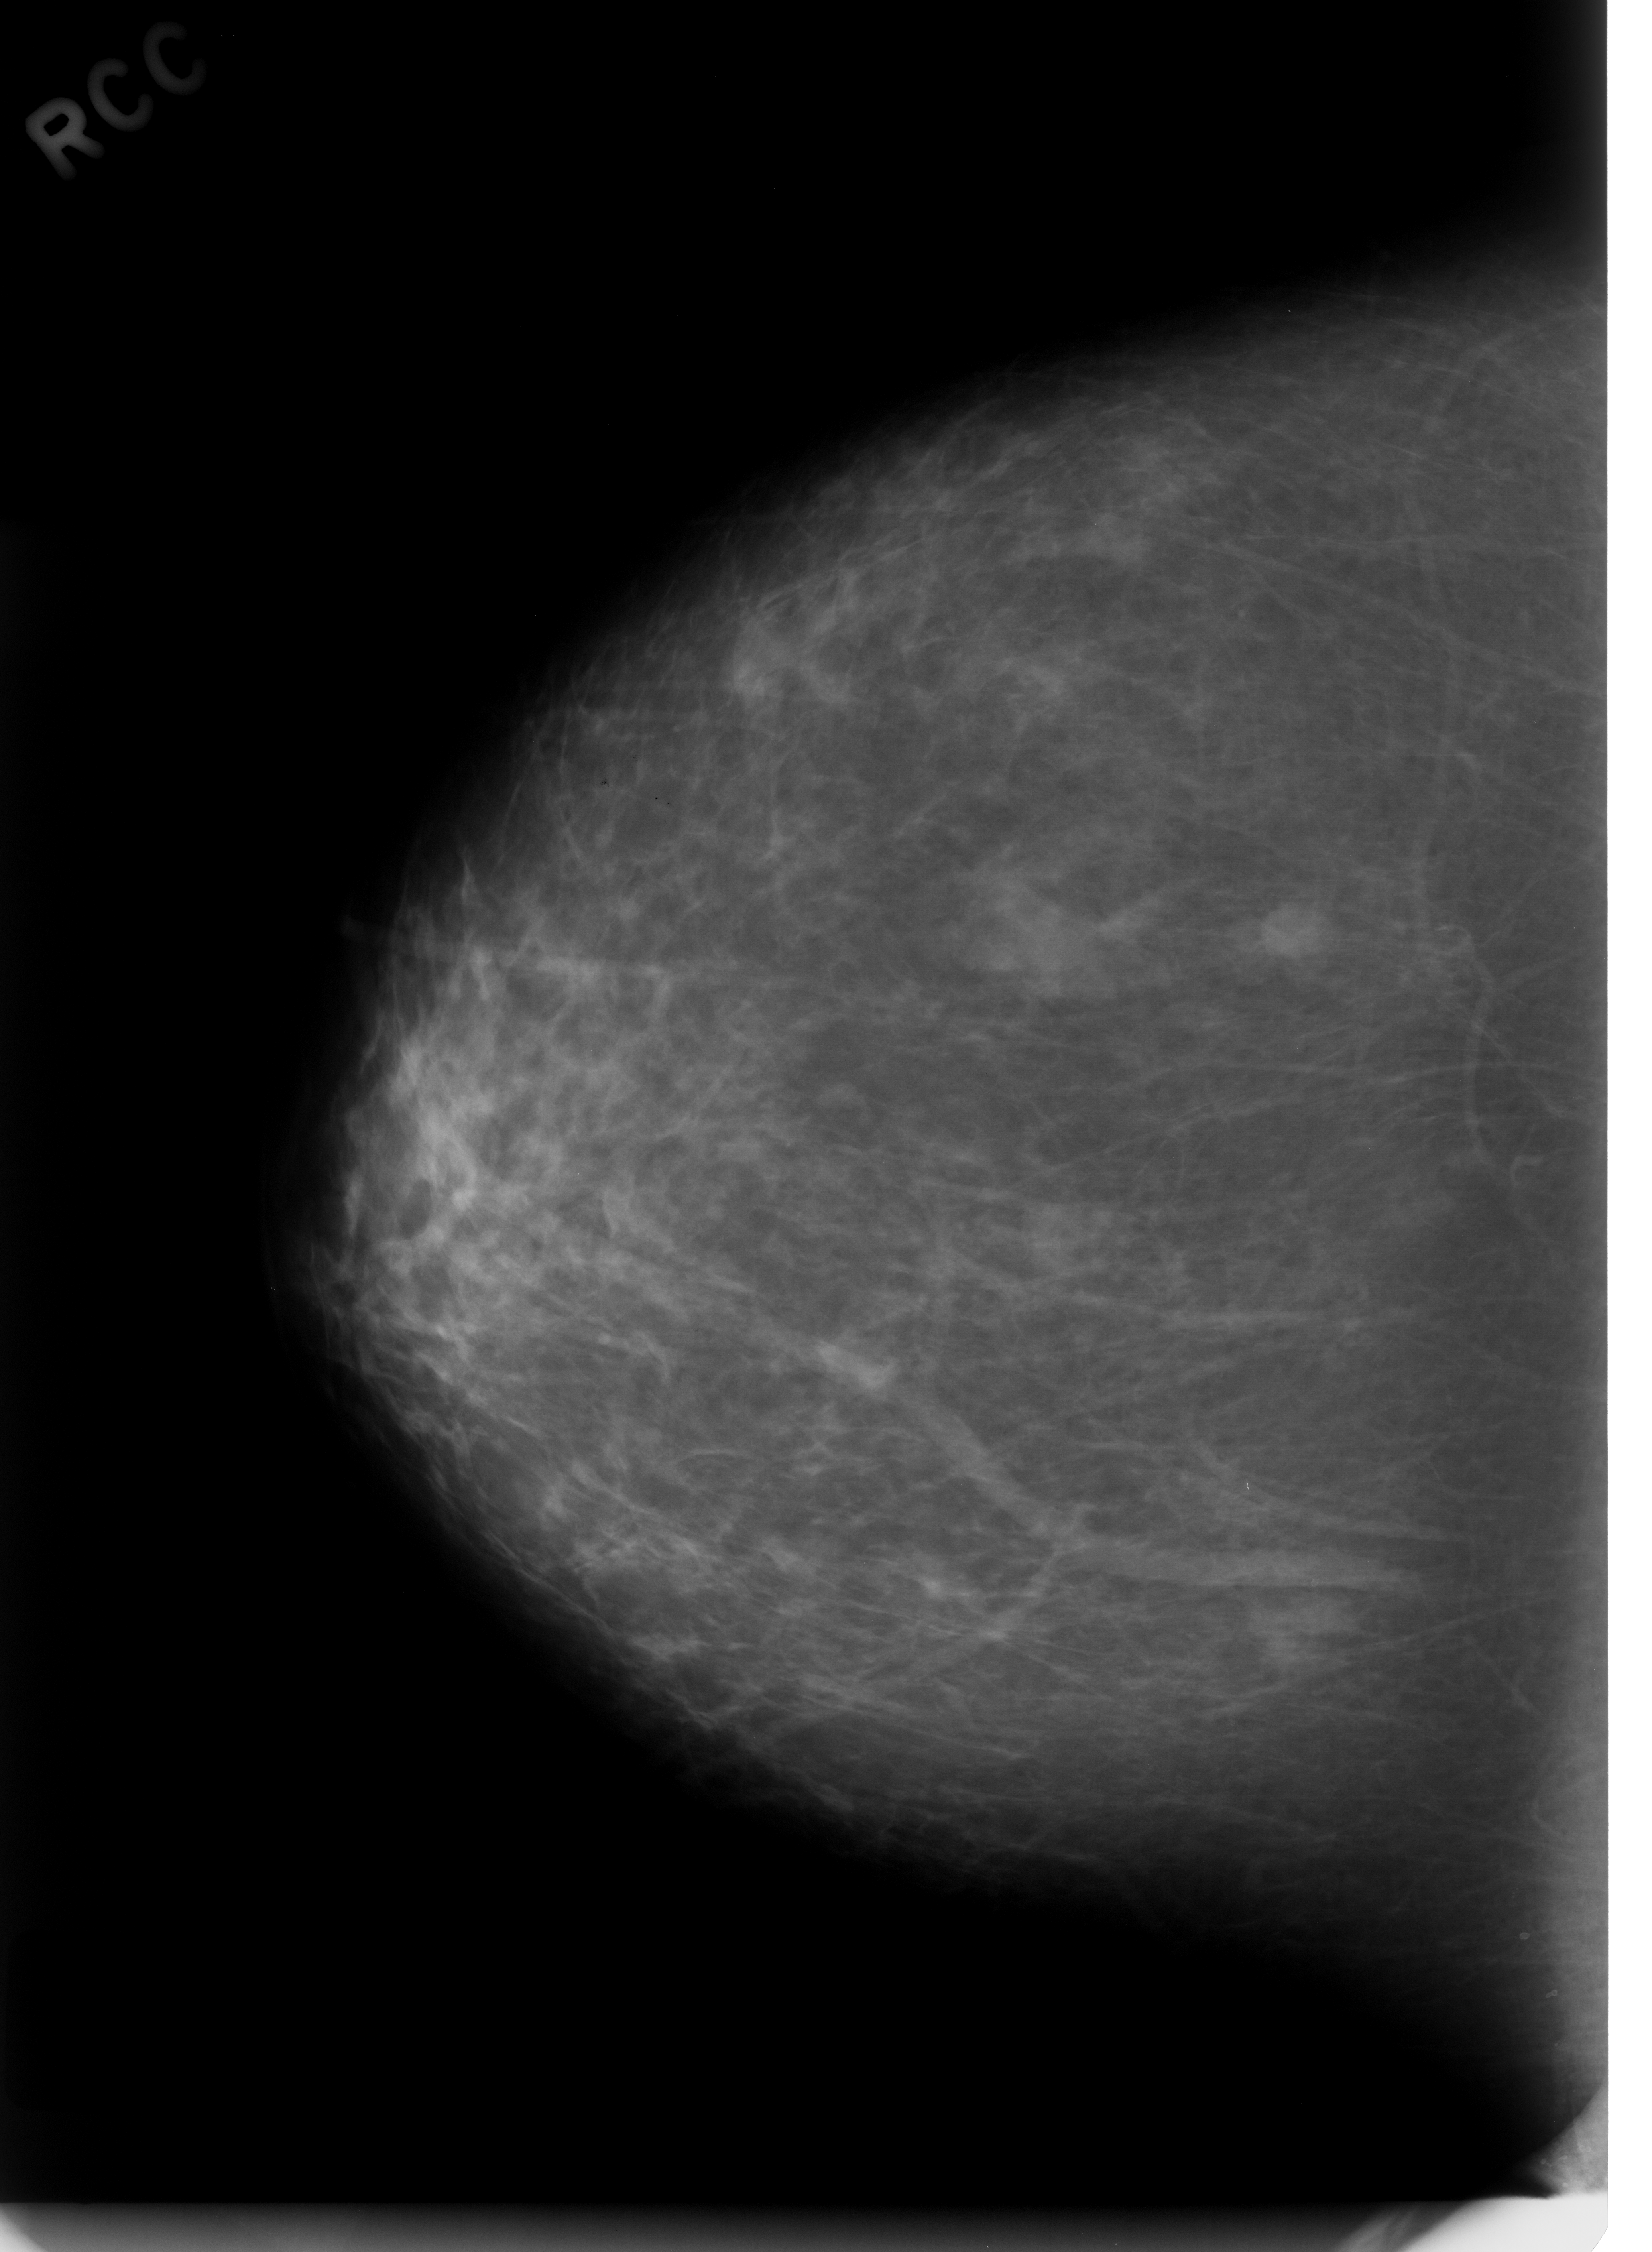
Digitized screen-film mammogram. Right breast. Craniocaudal (CC) view. Breast composition: almost entirely fatty (BI-RADS density category 1 of 4). 1652 × 2252 image matrix.
Expert-marked regions of interest on this film, with their recorded descriptors:
- mass, shape oval, margins circumscribed; BI-RADS assessment category 3; subtlety rating 5 on a 1 (subtle) to 5 (obvious) scale; pathology (as recorded): benign: bounding box <1224,893,1340,983> (left, top, right, bottom; pixels)